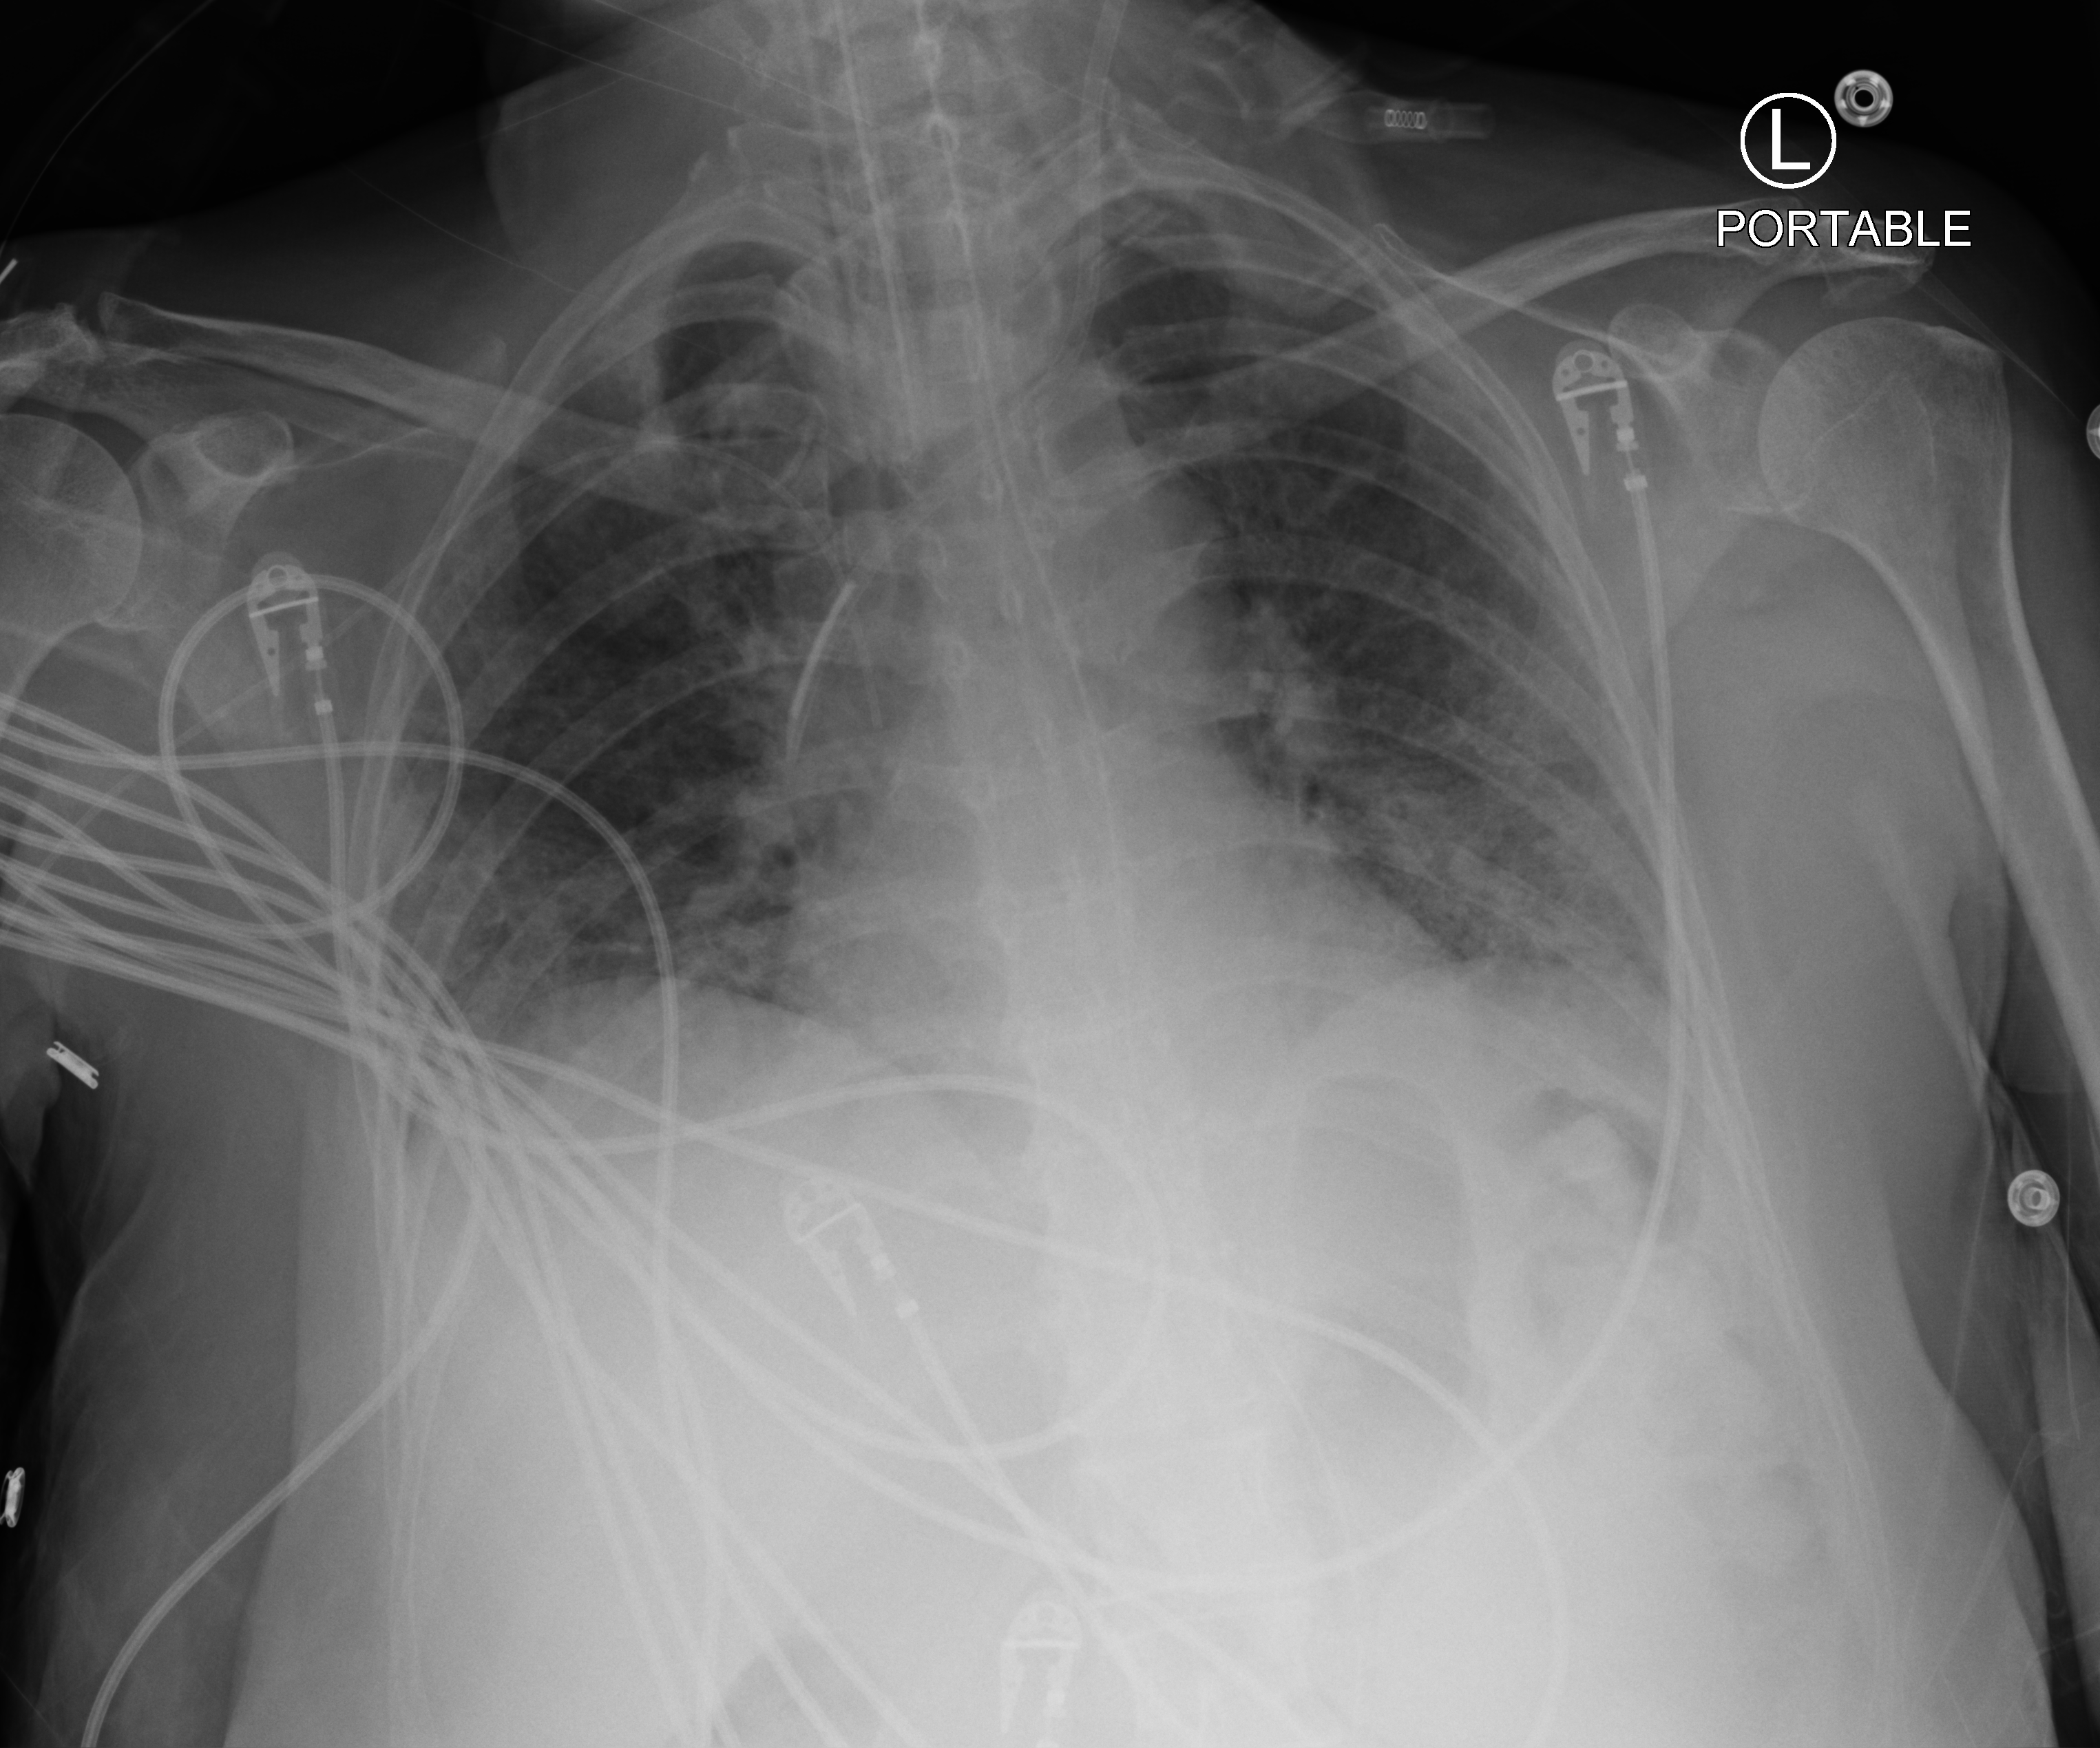
Portable chest radiograph, anteroposterior (AP) projection. Patient hospitalised with COVID-19; female, aged 60–74 years.
From the hospital-stay record, not from the radiograph (when in the stay this image was taken is not recorded): mechanically ventilated during this hospital stay: yes.